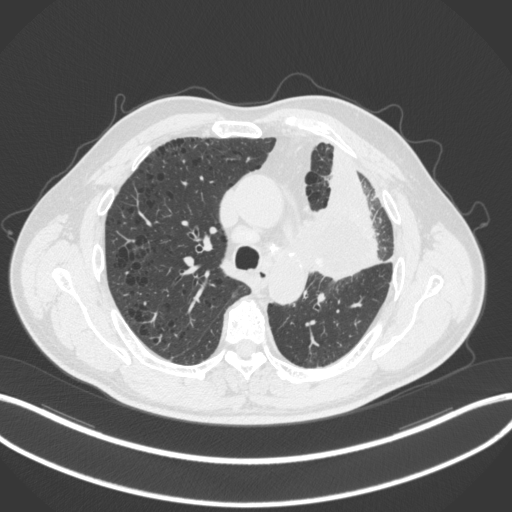
Chest CT, one axial slice; slice 198 of 286 in the series (ordered by position); lung window (W 1500 / L -600 HU); 1 mm slice thickness; 512 × 512 image matrix, field of view 400 × 400 mm. Patient: male, 68 years. From the clinical record (not read from this slice): clinical TNM (as recorded): T3 N3 M1.
Structures marked on this image (bounding box drawn by a radiologist):
- lung tumour (recorded histology: adenocarcinoma): box from (x=293, y=193) to (x=393, y=288) px